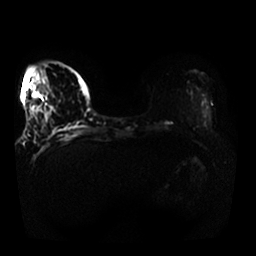
Breast MRI, one axial slice. Slice 8 of 25 in the series (ordered by position). Diffusion-weighted series; image 2 of 4 stored at this slice position (different b-values; order by instance number). 1.5 T. 256 × 256 image matrix. Female patient.
Annotated regions visible in this slice (outlined manually by an expert reader):
- tumour on diffusion-weighted imaging: bounding box (x1, y1, x2, y2) in pixels: (34, 92, 51, 117)